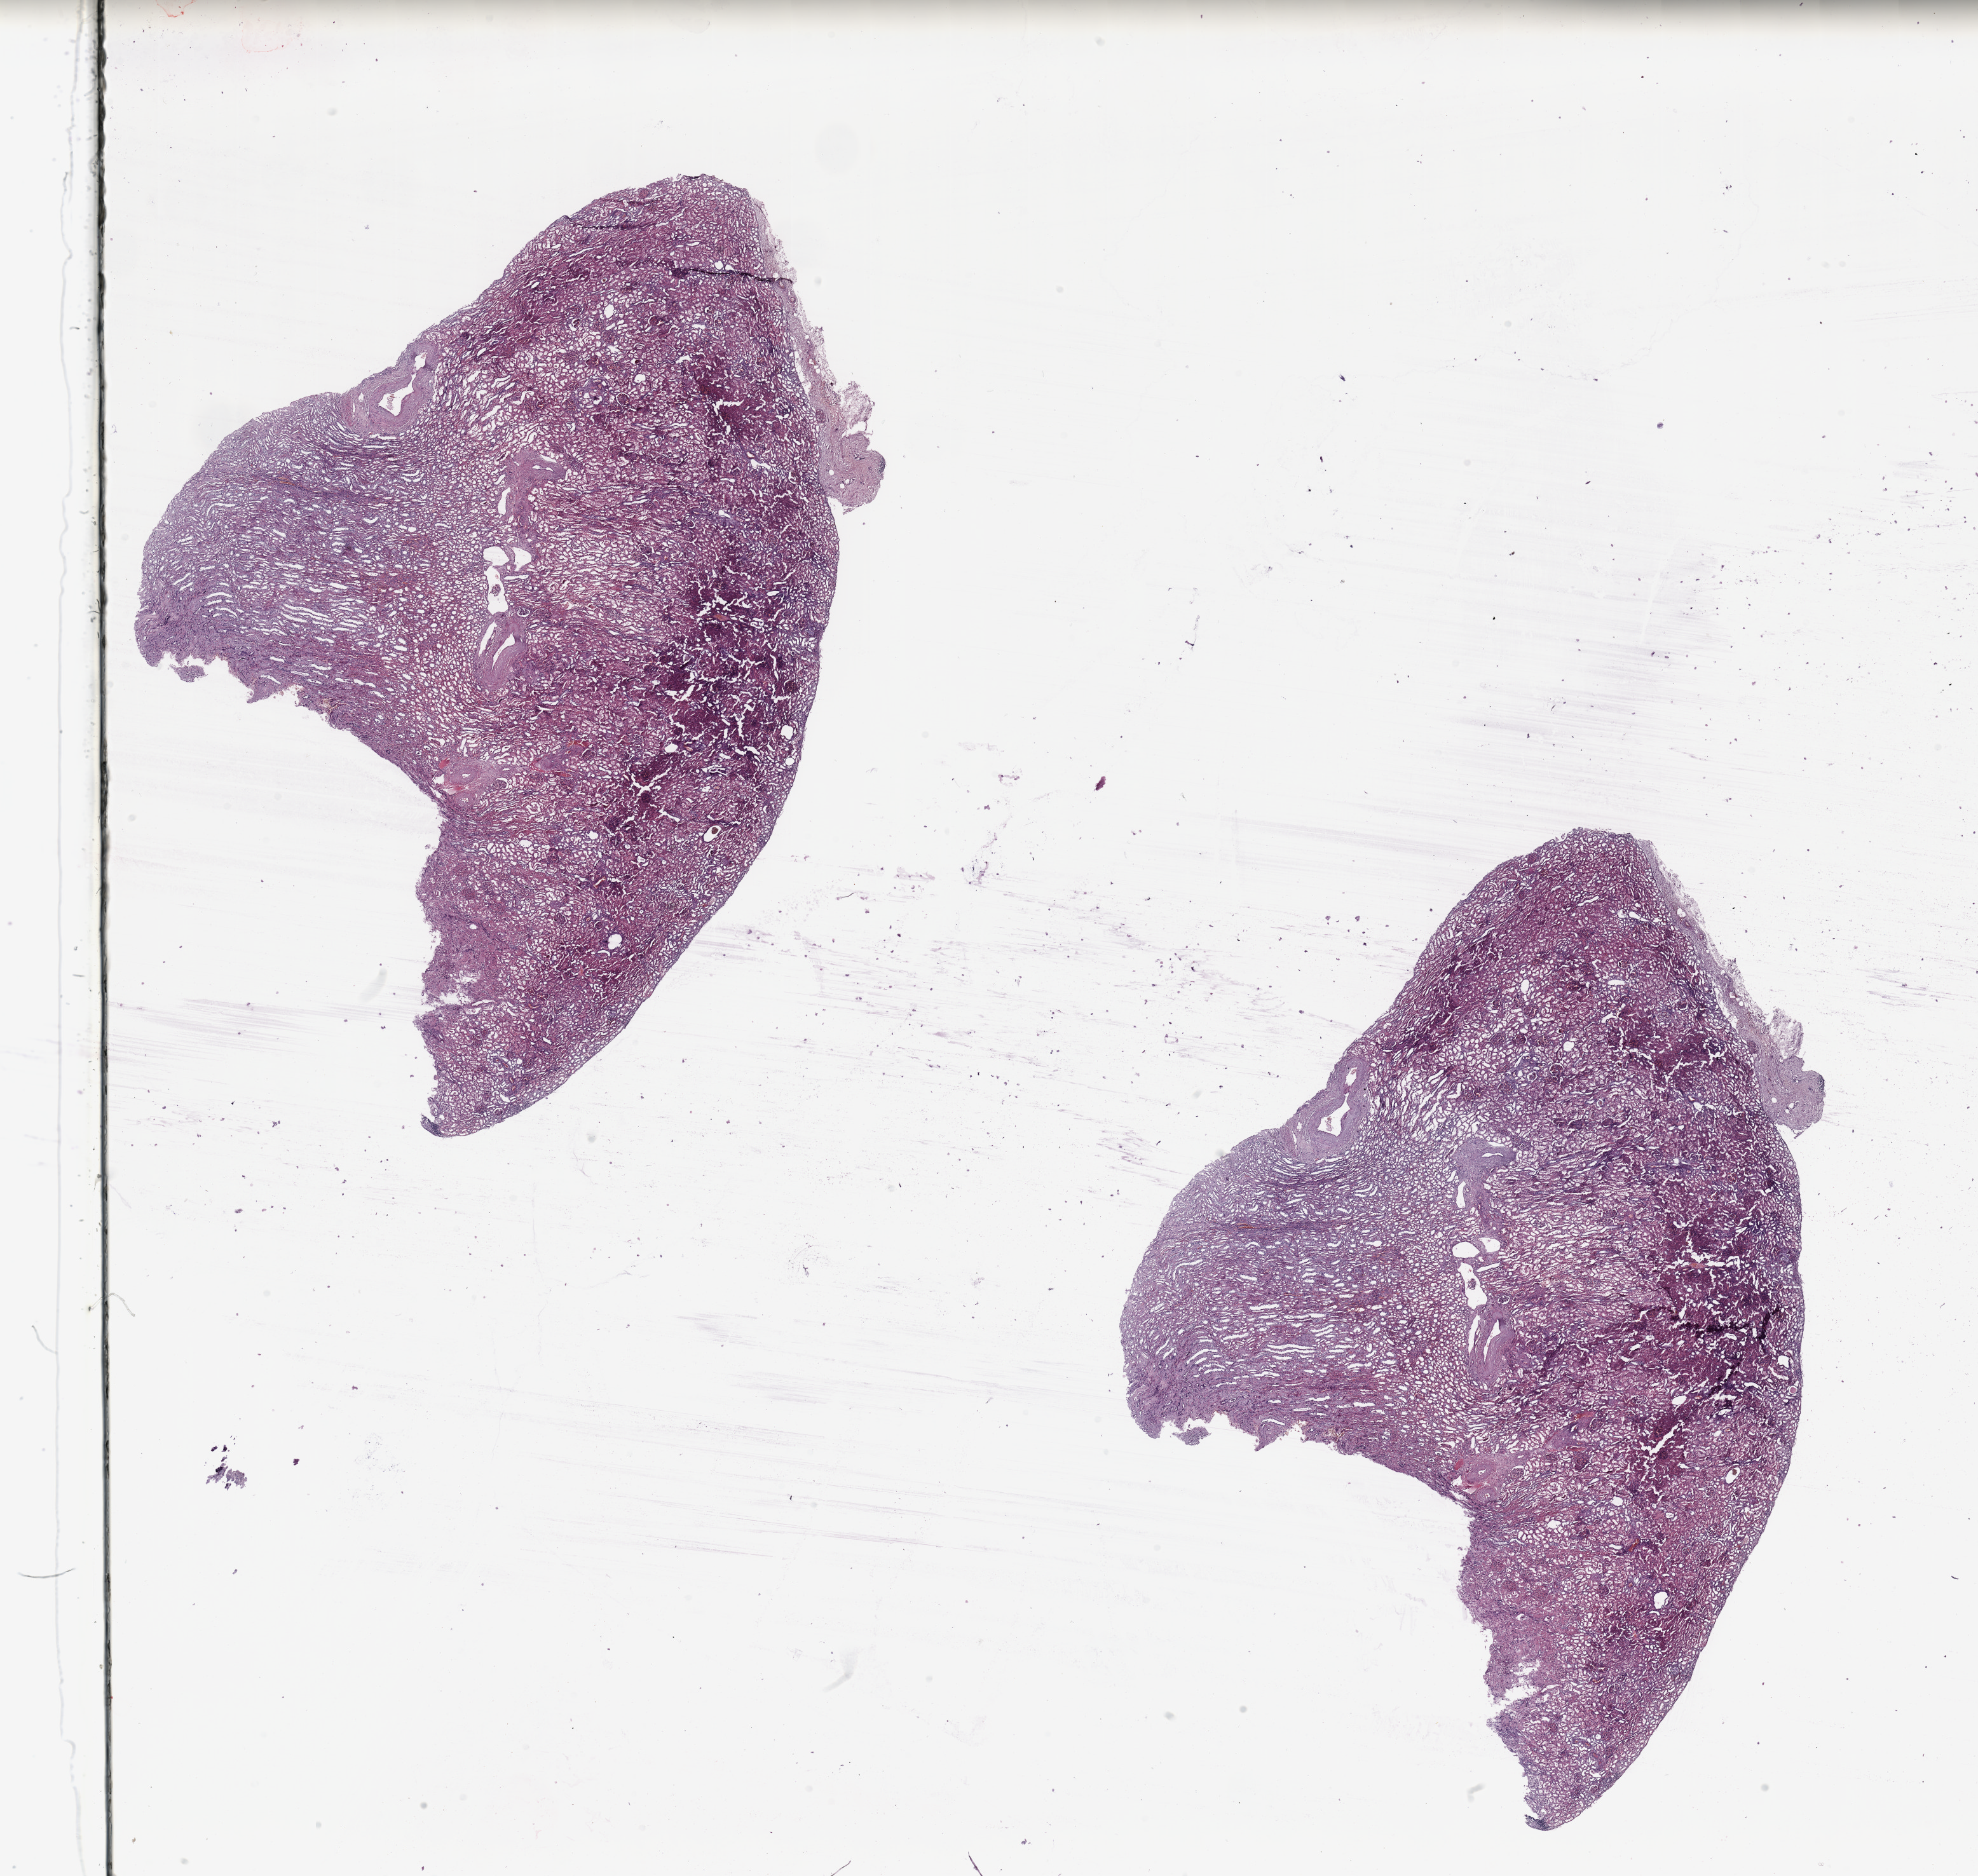
H&E-stained whole-slide image, a low-resolution overview of the entire scanned area, about 24.6 x 23.3 mm (from a 20x scan), normal (non-tumour) tissue sample, sampled site: kidney. Patient: female, age 66 years.
This section: normal (non-tumour) tissue from the same patient. Patient diagnosis: Renal cell carcinoma, NOS.